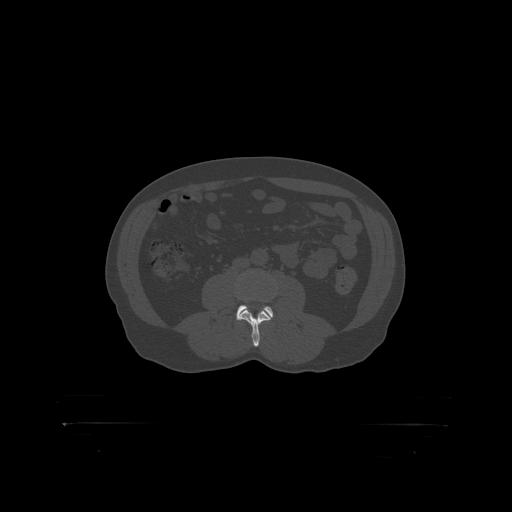
CT including the spine, one axial slice. Position 254 of 399 along the scan axis. Reconstruction kernel STANDARD. 120 kVp. Bone window (W 1800 / L 400 HU). 1.25 mm slice thickness. 512 × 512 image matrix, field of view 650 × 650 mm. Male patient, age 46 years. Case-level facts recorded for this patient, not image findings: primary cancer: skin.
Outlined on this slice (semi-automatically segmented with operator editing):
- L3 vertebra: bounding box (x1, y1, x2, y2) in pixels: (240, 309, 270, 319)
- L4 vertebra: (236, 305, 274, 317)